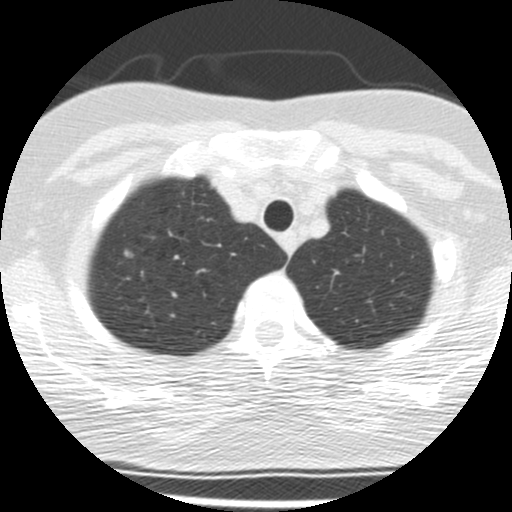
Low-dose screening chest CT, axial slice. Baseline annual screen. Lung window (W 1500 / L -600 HU). Standard (soft-tissue) reconstruction kernel (STANDARD). Slice 35 of 190 in the series. 512 × 512 image matrix. Female, age 56 years at enrolment. Current smoker at enrolment.
Expert-annotated lung lesion, bounding box [x1, y1, x2, y2] px = [111, 238, 153, 275]. Reader record for this screening exam (exam-level; its link to the box is not recorded): non-calcified nodule or mass ≥4 mm, right upper lobe, 6 × 6 mm, smooth margins, soft tissue attenuation.